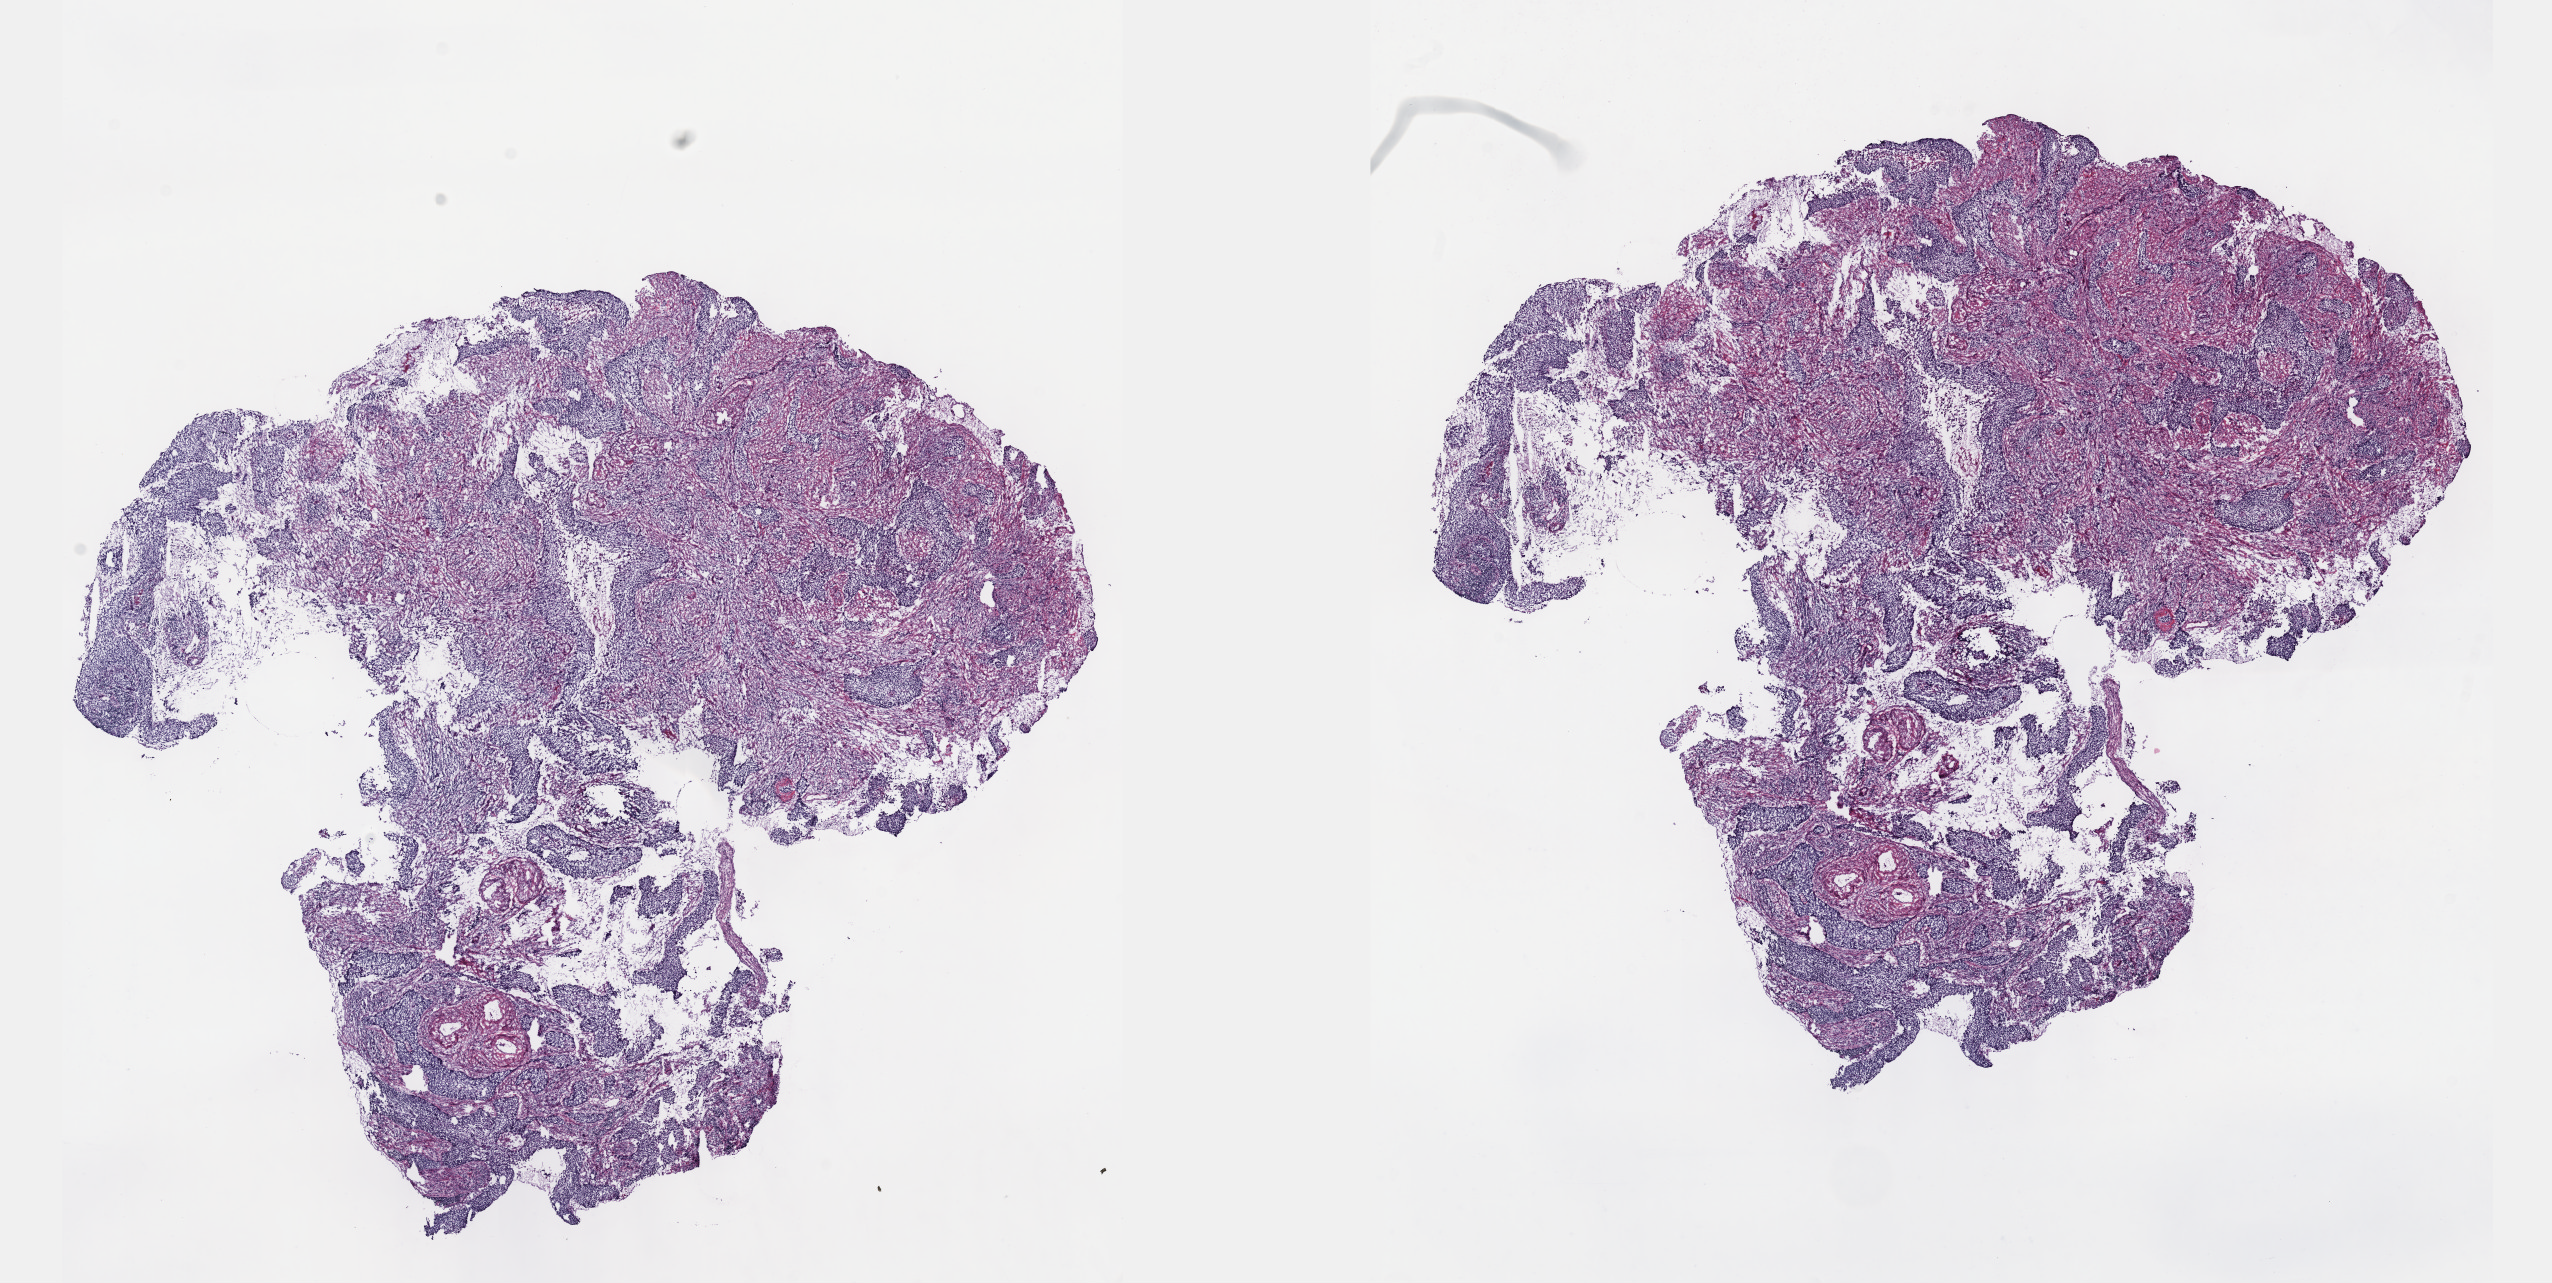
Hematoxylin and eosin (H&E) stained whole-slide image — low-resolution overview of the scanned area, about 20.6 x 10.4 mm (slide scanned at 40x), frozen section, sample: primary tumour, cervix. Female, age 35 years at initial diagnosis. Histologic grade: G2 (moderately differentiated). Pathologist review of this section (percent, as recorded): tumour cells 60%, tumour nuclei 70%, normal cells 0%, stromal cells 40%, necrosis 0%. Inflammatory infiltration, as recorded: lymphocyte infiltration 0%, monocyte infiltration 0%, neutrophil infiltration 0%.
Pathologic diagnosis: Squamous cell carcinoma, large cell, nonkeratinizing, NOS. FIGO stage: IIIB.